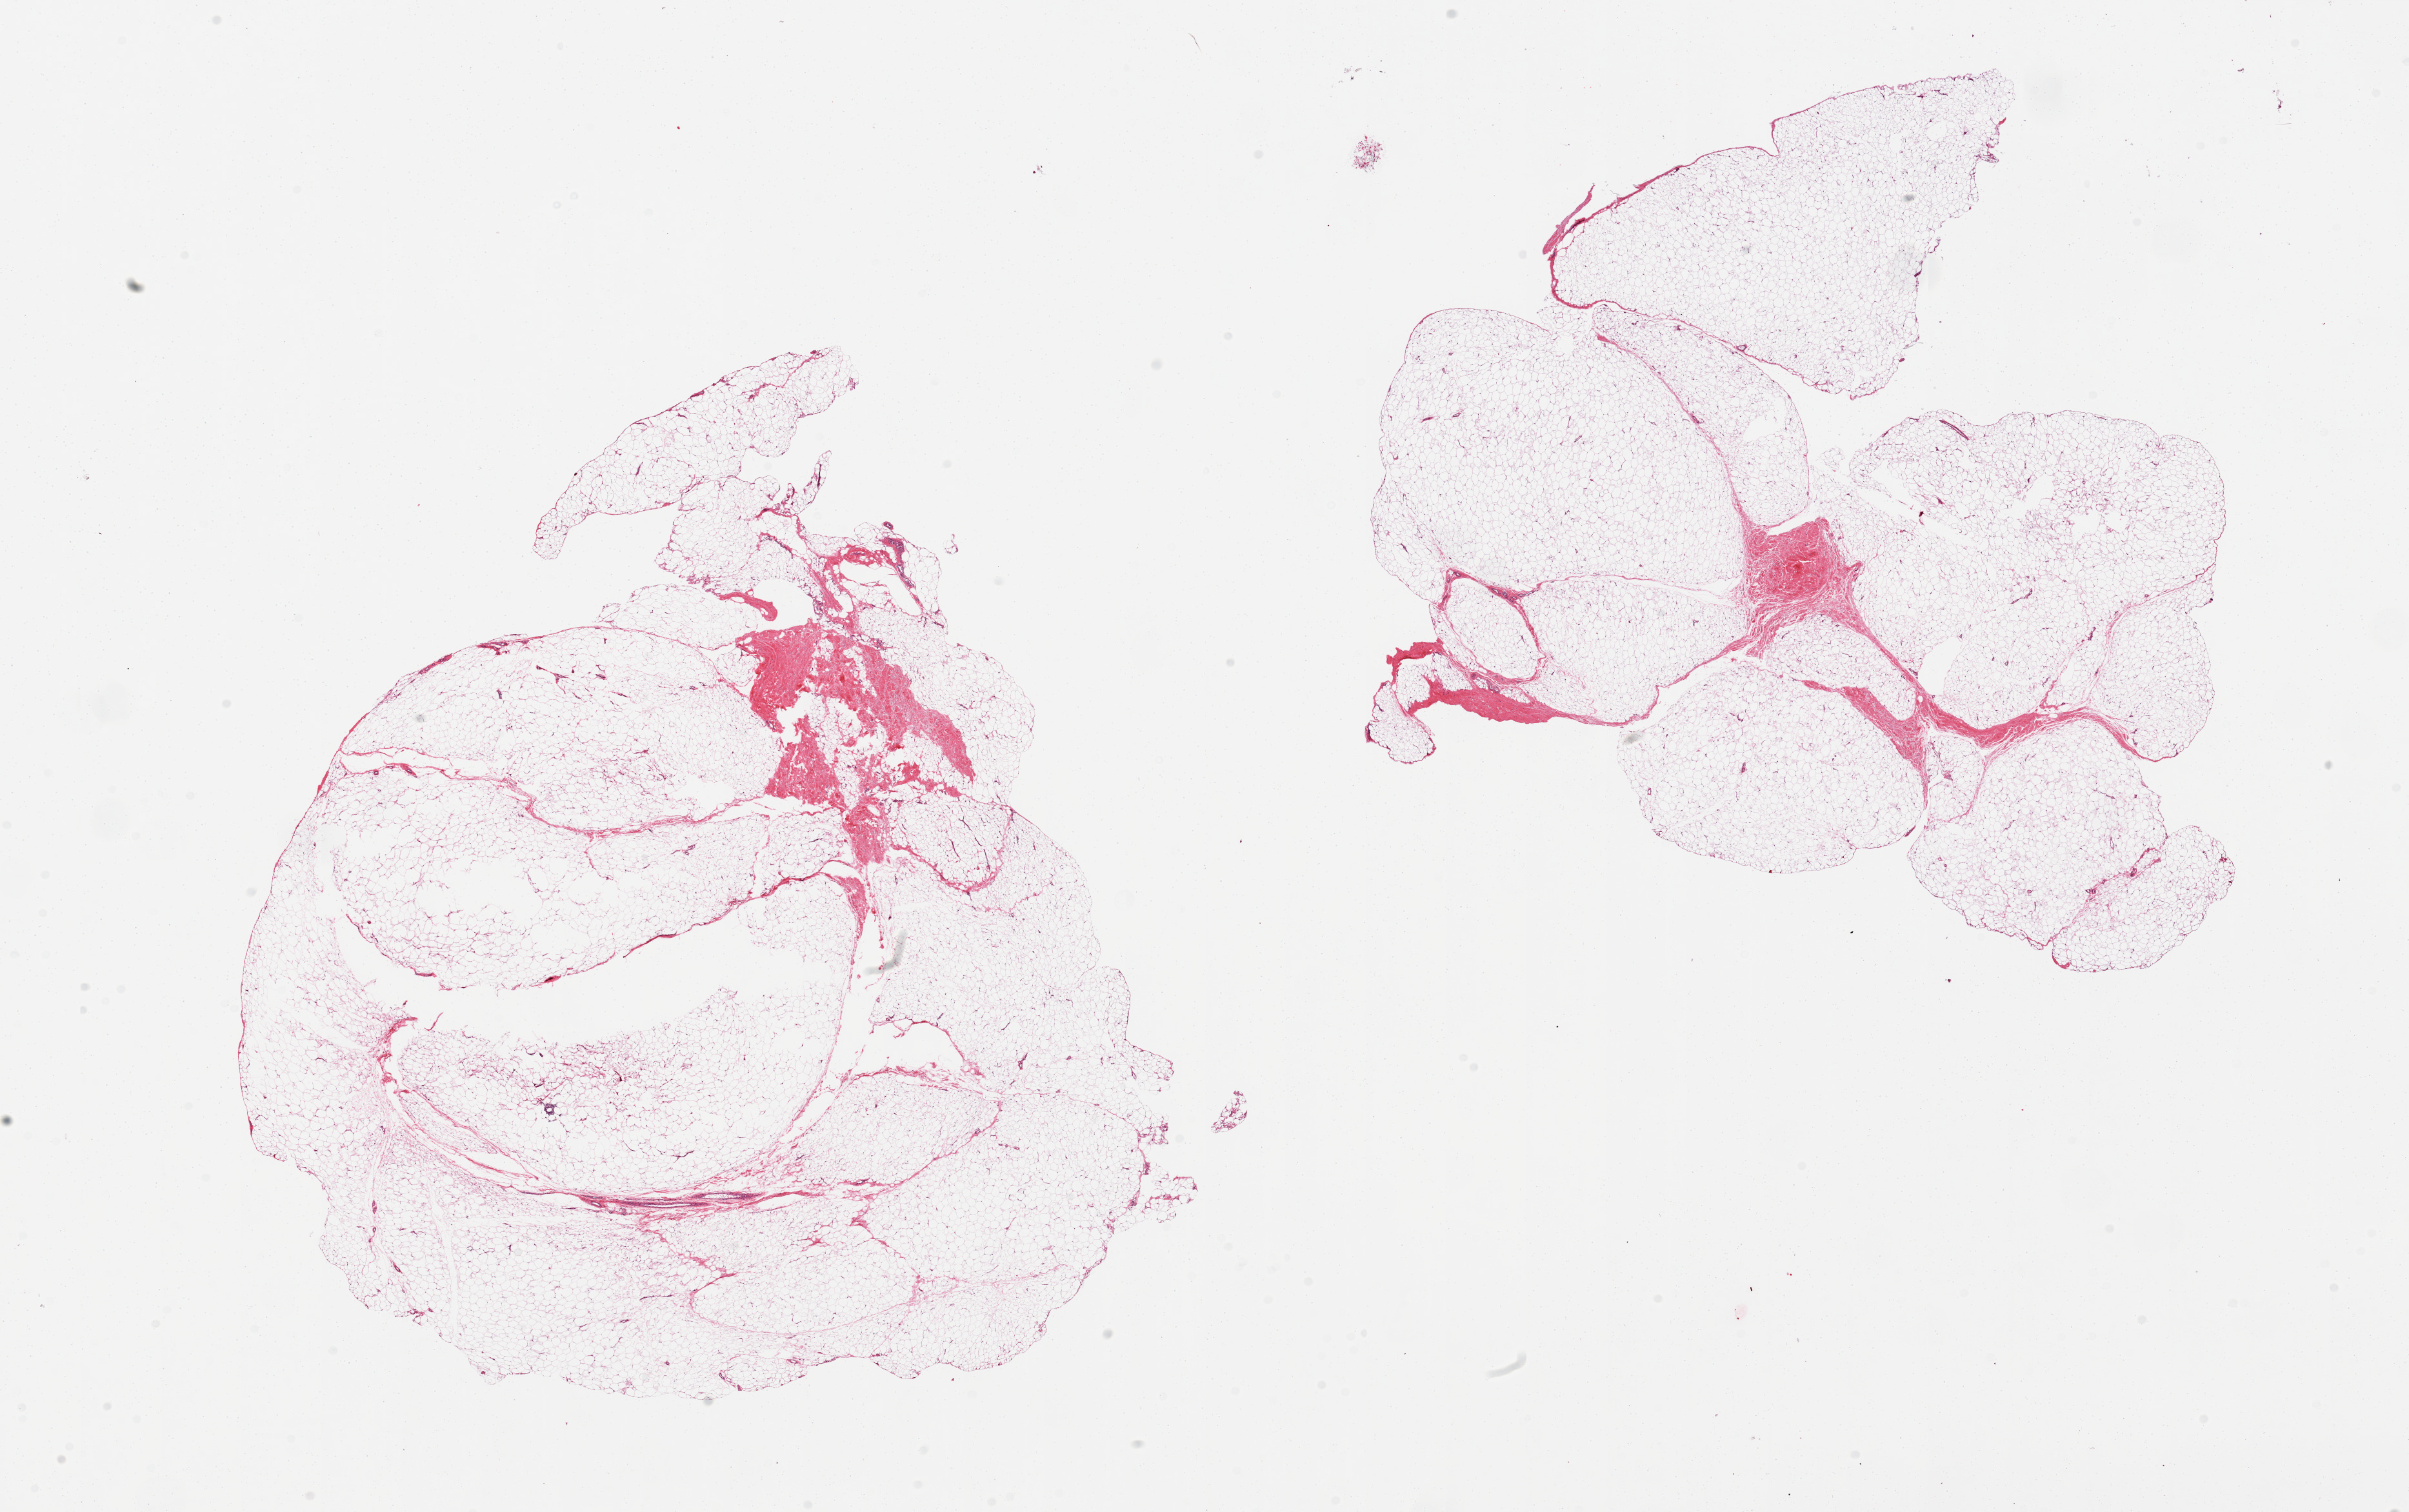
H&E whole-slide image — low-resolution overview of the scanned area, about 29.5 x 18.5 mm (from a 20x scan), PAXgene-fixed, paraffin-embedded tissue, sampled site (target tissue): adipose tissue, tissue donor sample. Donor: male.
Review note (as recorded): 2 pieces.